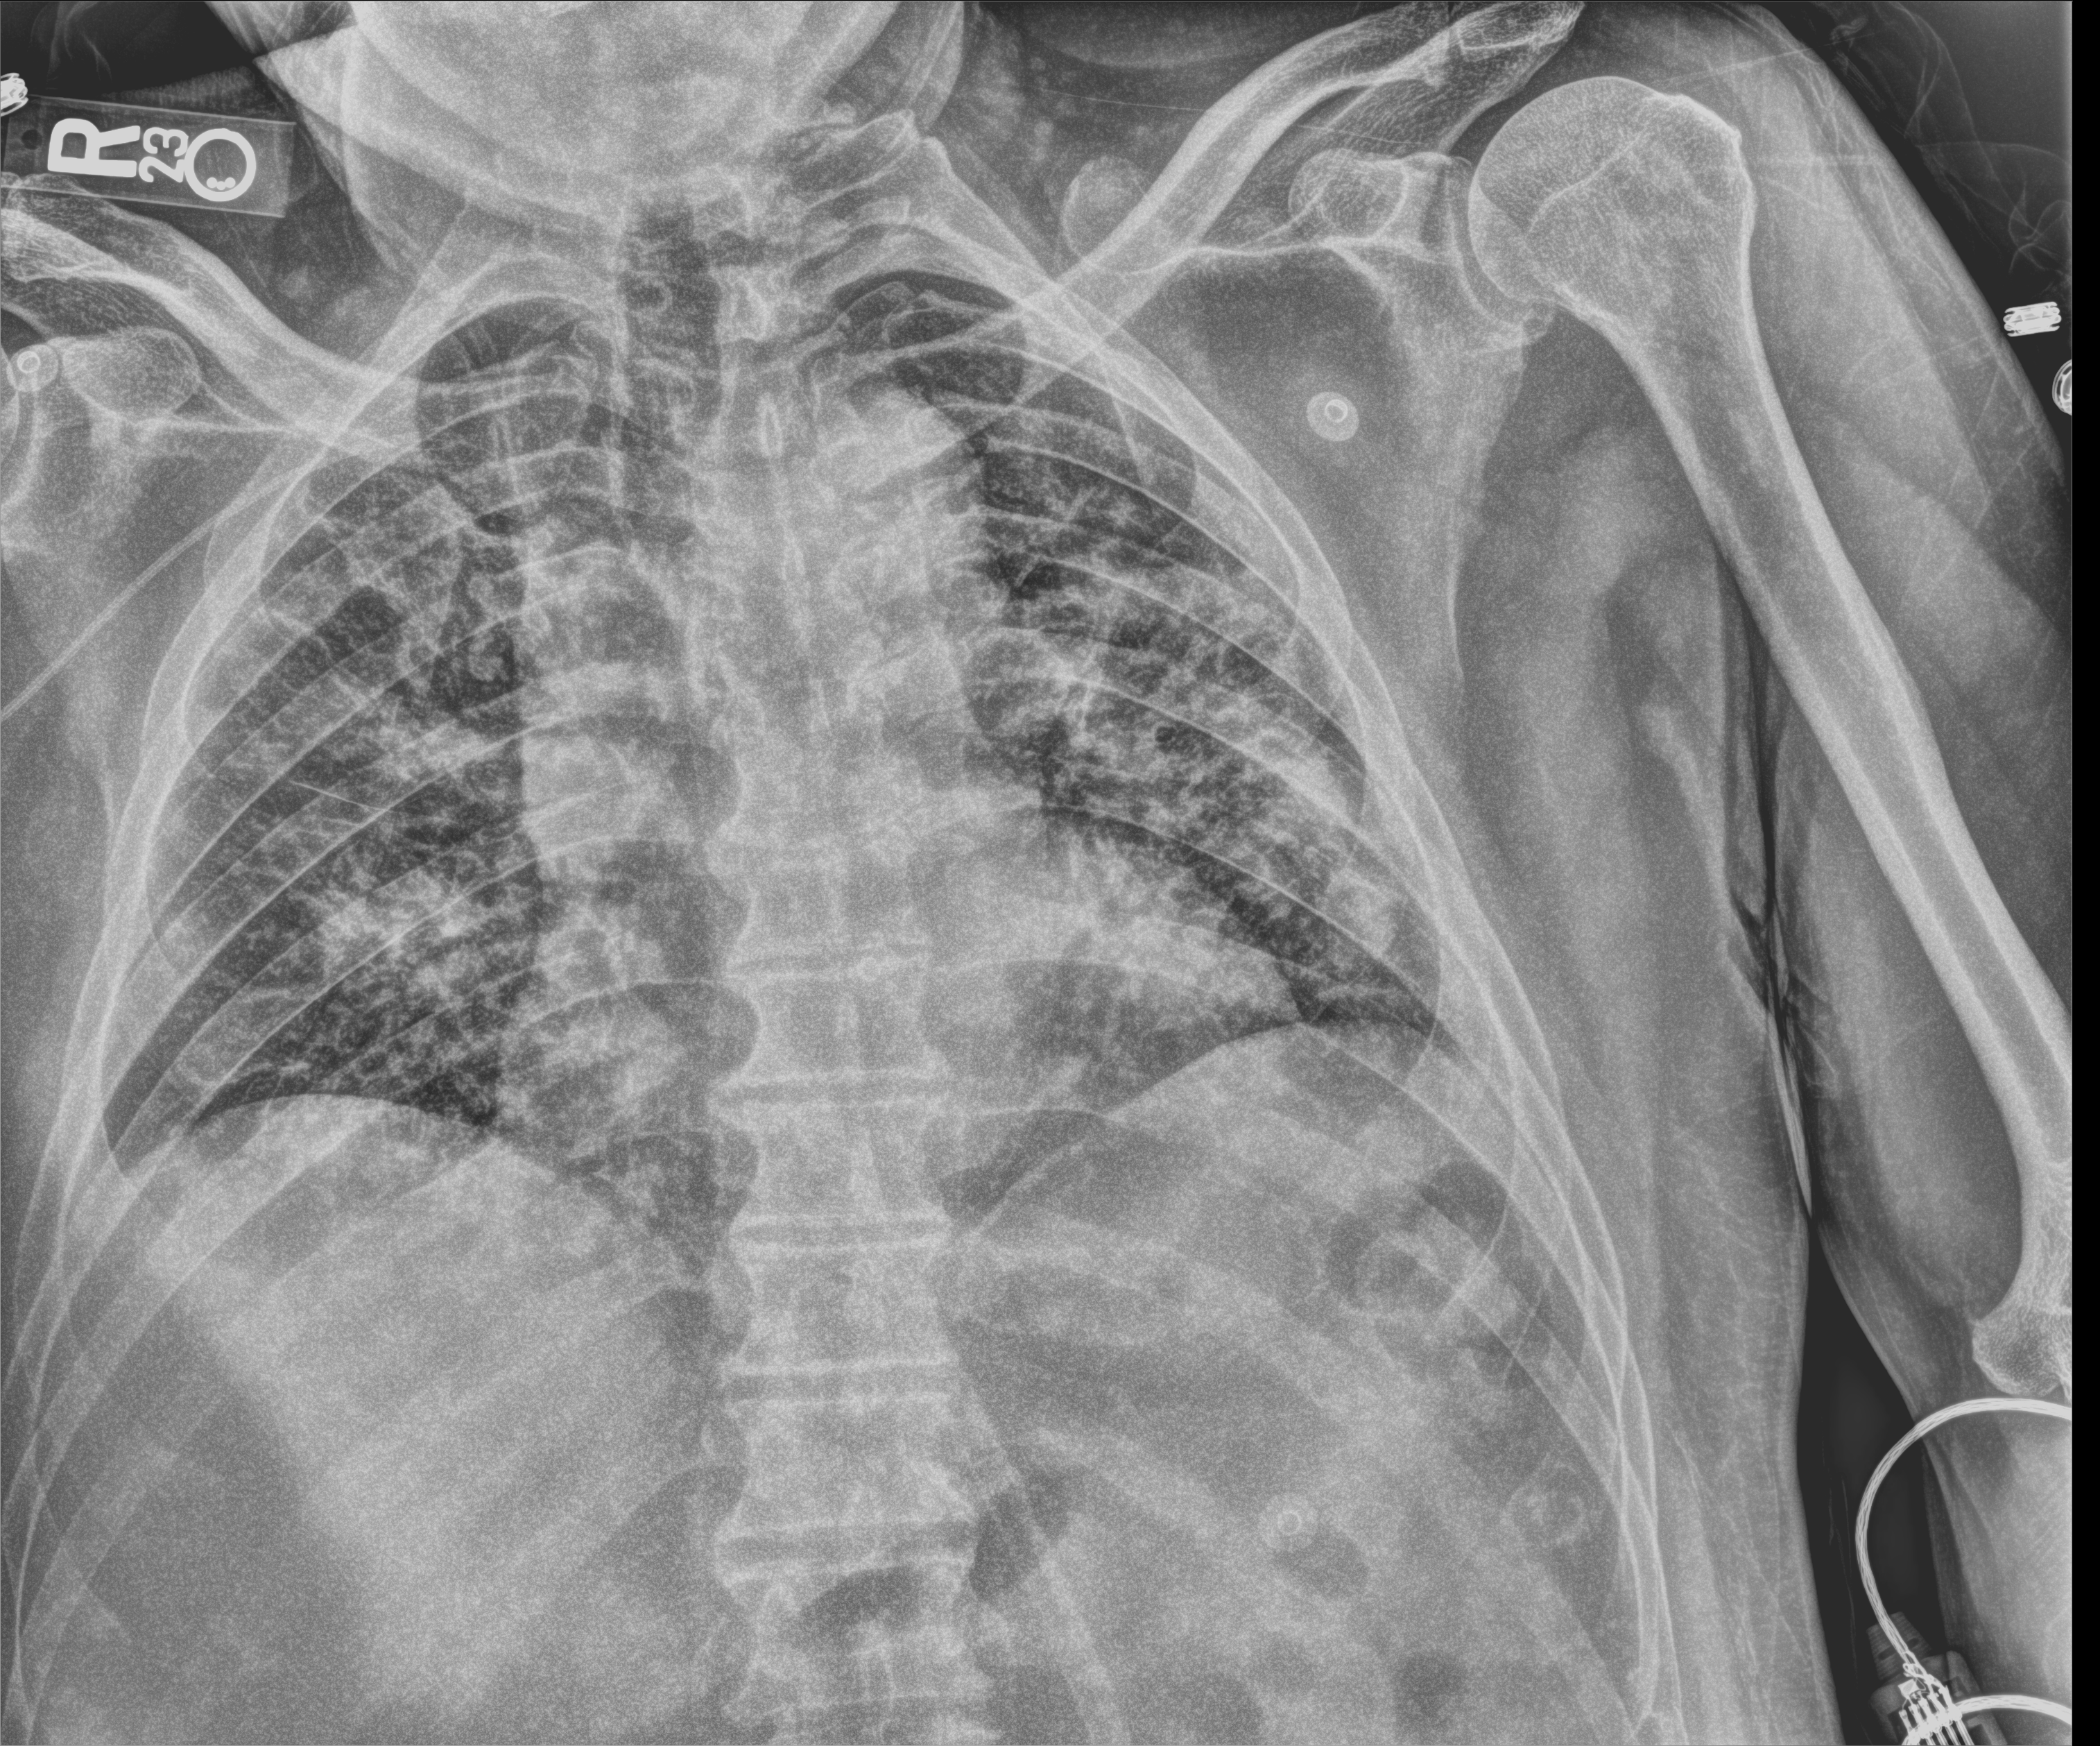
Chest X-ray (portable); anteroposterior (AP) projection. Male patient hospitalised with COVID-19, age 60–74 years.
Admission-level facts for this patient (not findings on this image; timing relative to this image not recorded): length of hospital stay: 20 days; mechanically ventilated during this hospital stay: yes; admitted to intensive care during this hospital stay: yes.